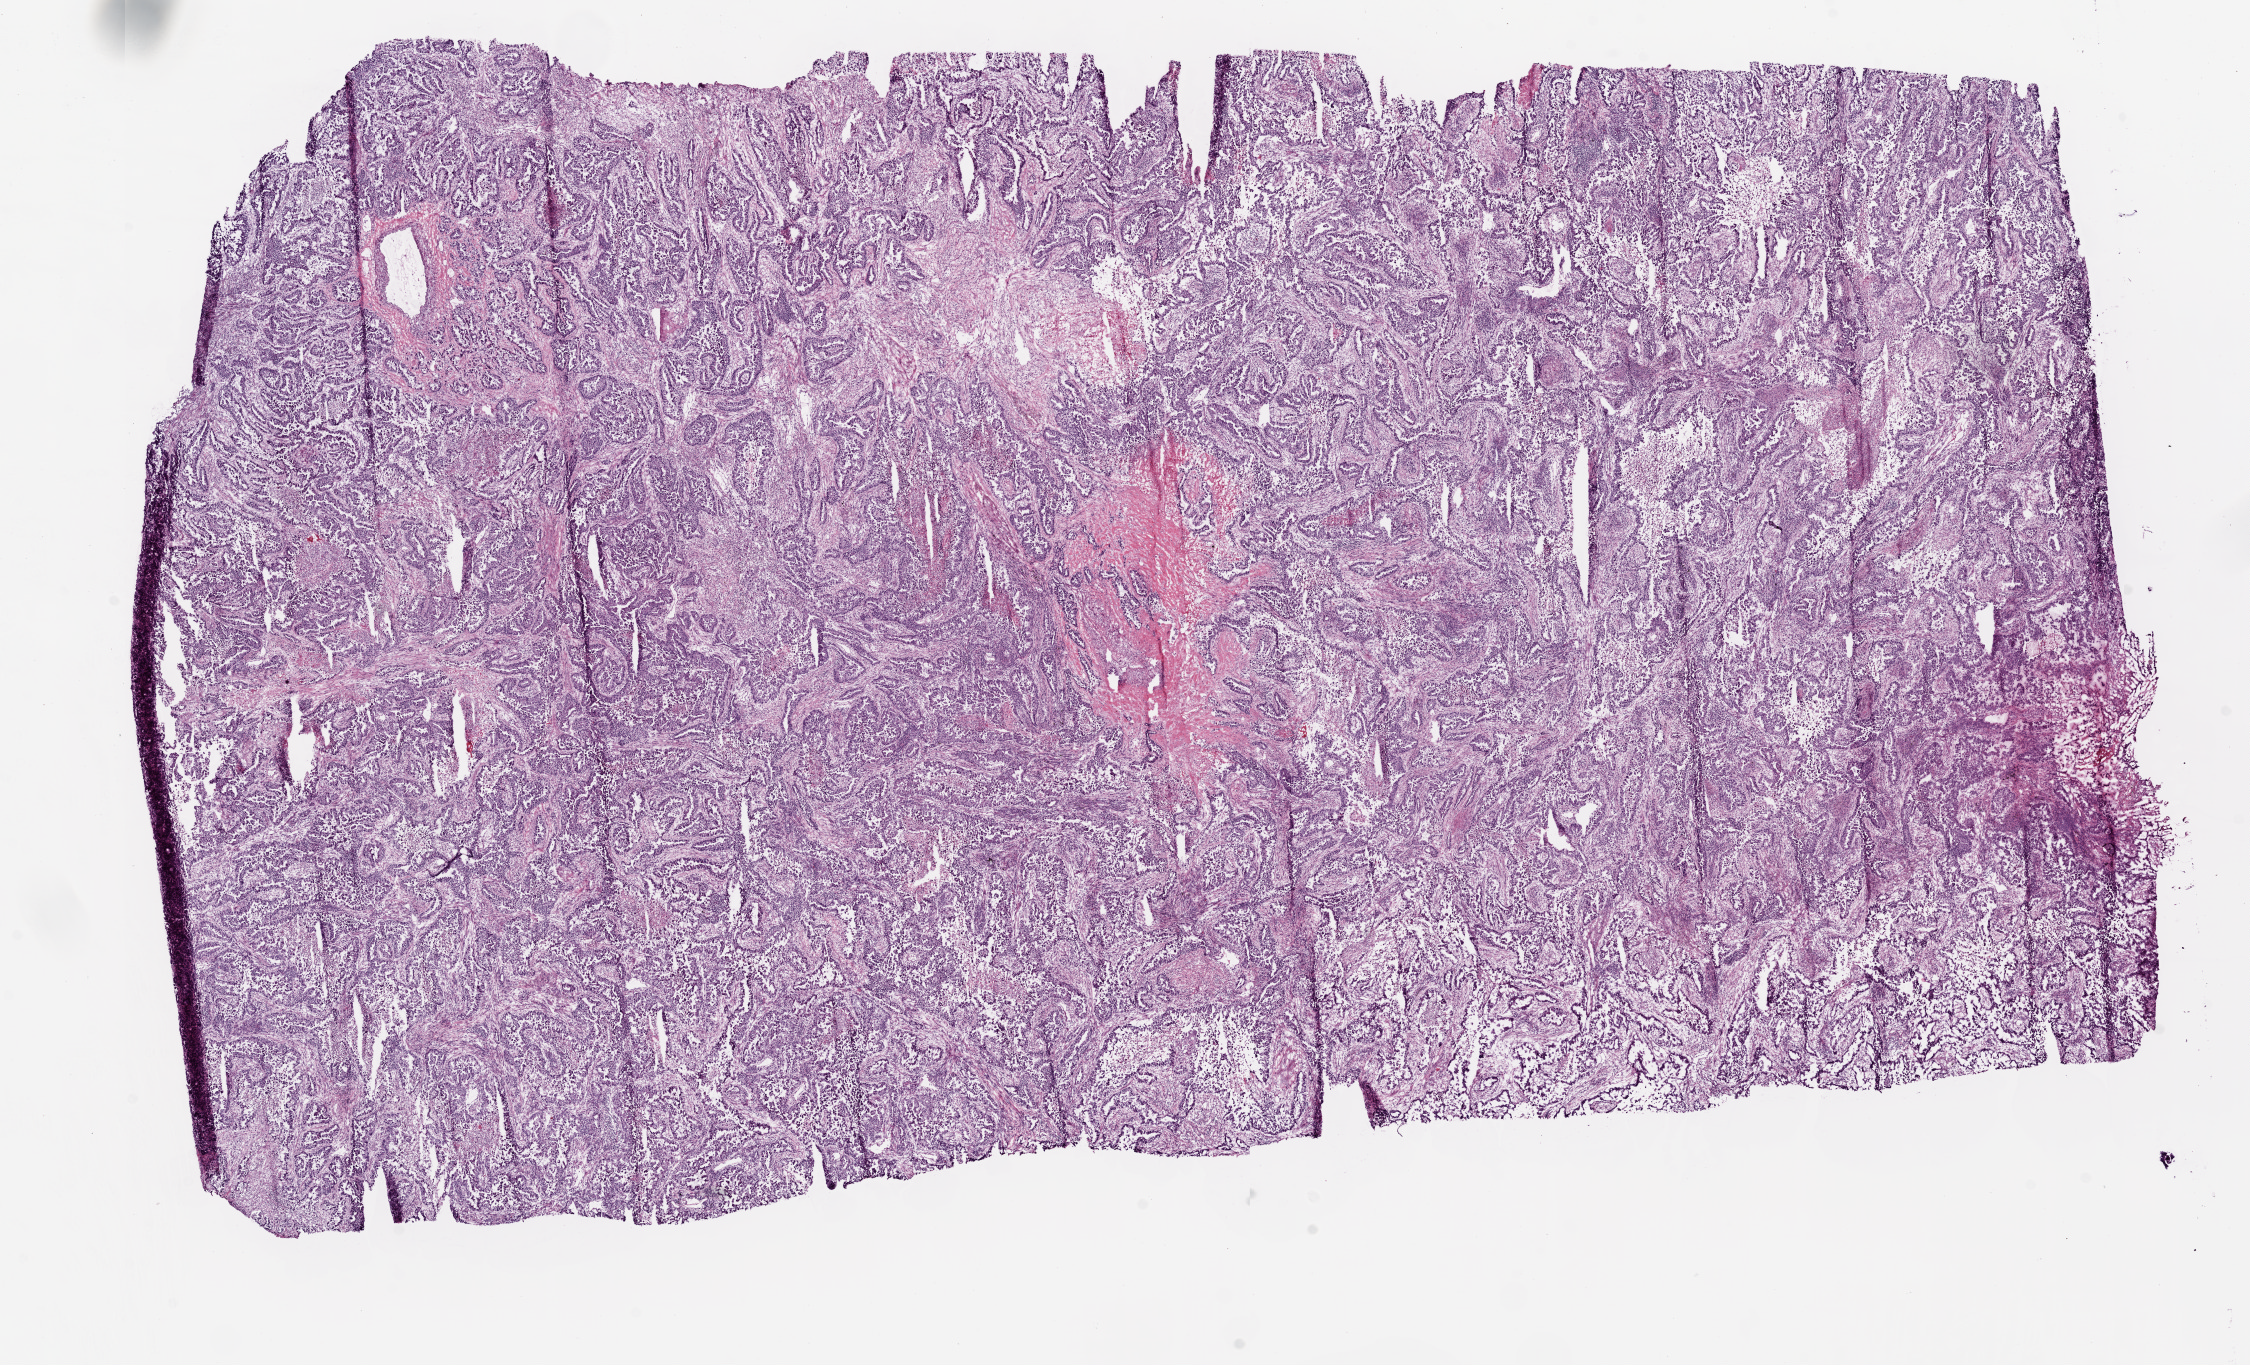
Digitized H&E tissue section (whole slide) — shown as a low-resolution overview of the whole scanned area (about 18.1 x 11.0 mm). Frozen section. Sample: primary tumour, lung. Female patient; age at initial diagnosis 58 years. Pathologist review of this section (percent, as recorded): tumour cells 70%, tumour nuclei 73%, normal cells 0%, stromal cells 20%, necrosis 10%. Infiltration values recorded for this section: lymphocyte infiltration 10%.
TNM: T2 N0 M0. Laterality: right. AJCC pathologic stage: IB (5th edition). Histologic diagnosis: Adenocarcinoma with mixed subtypes (upper lobe, lung).